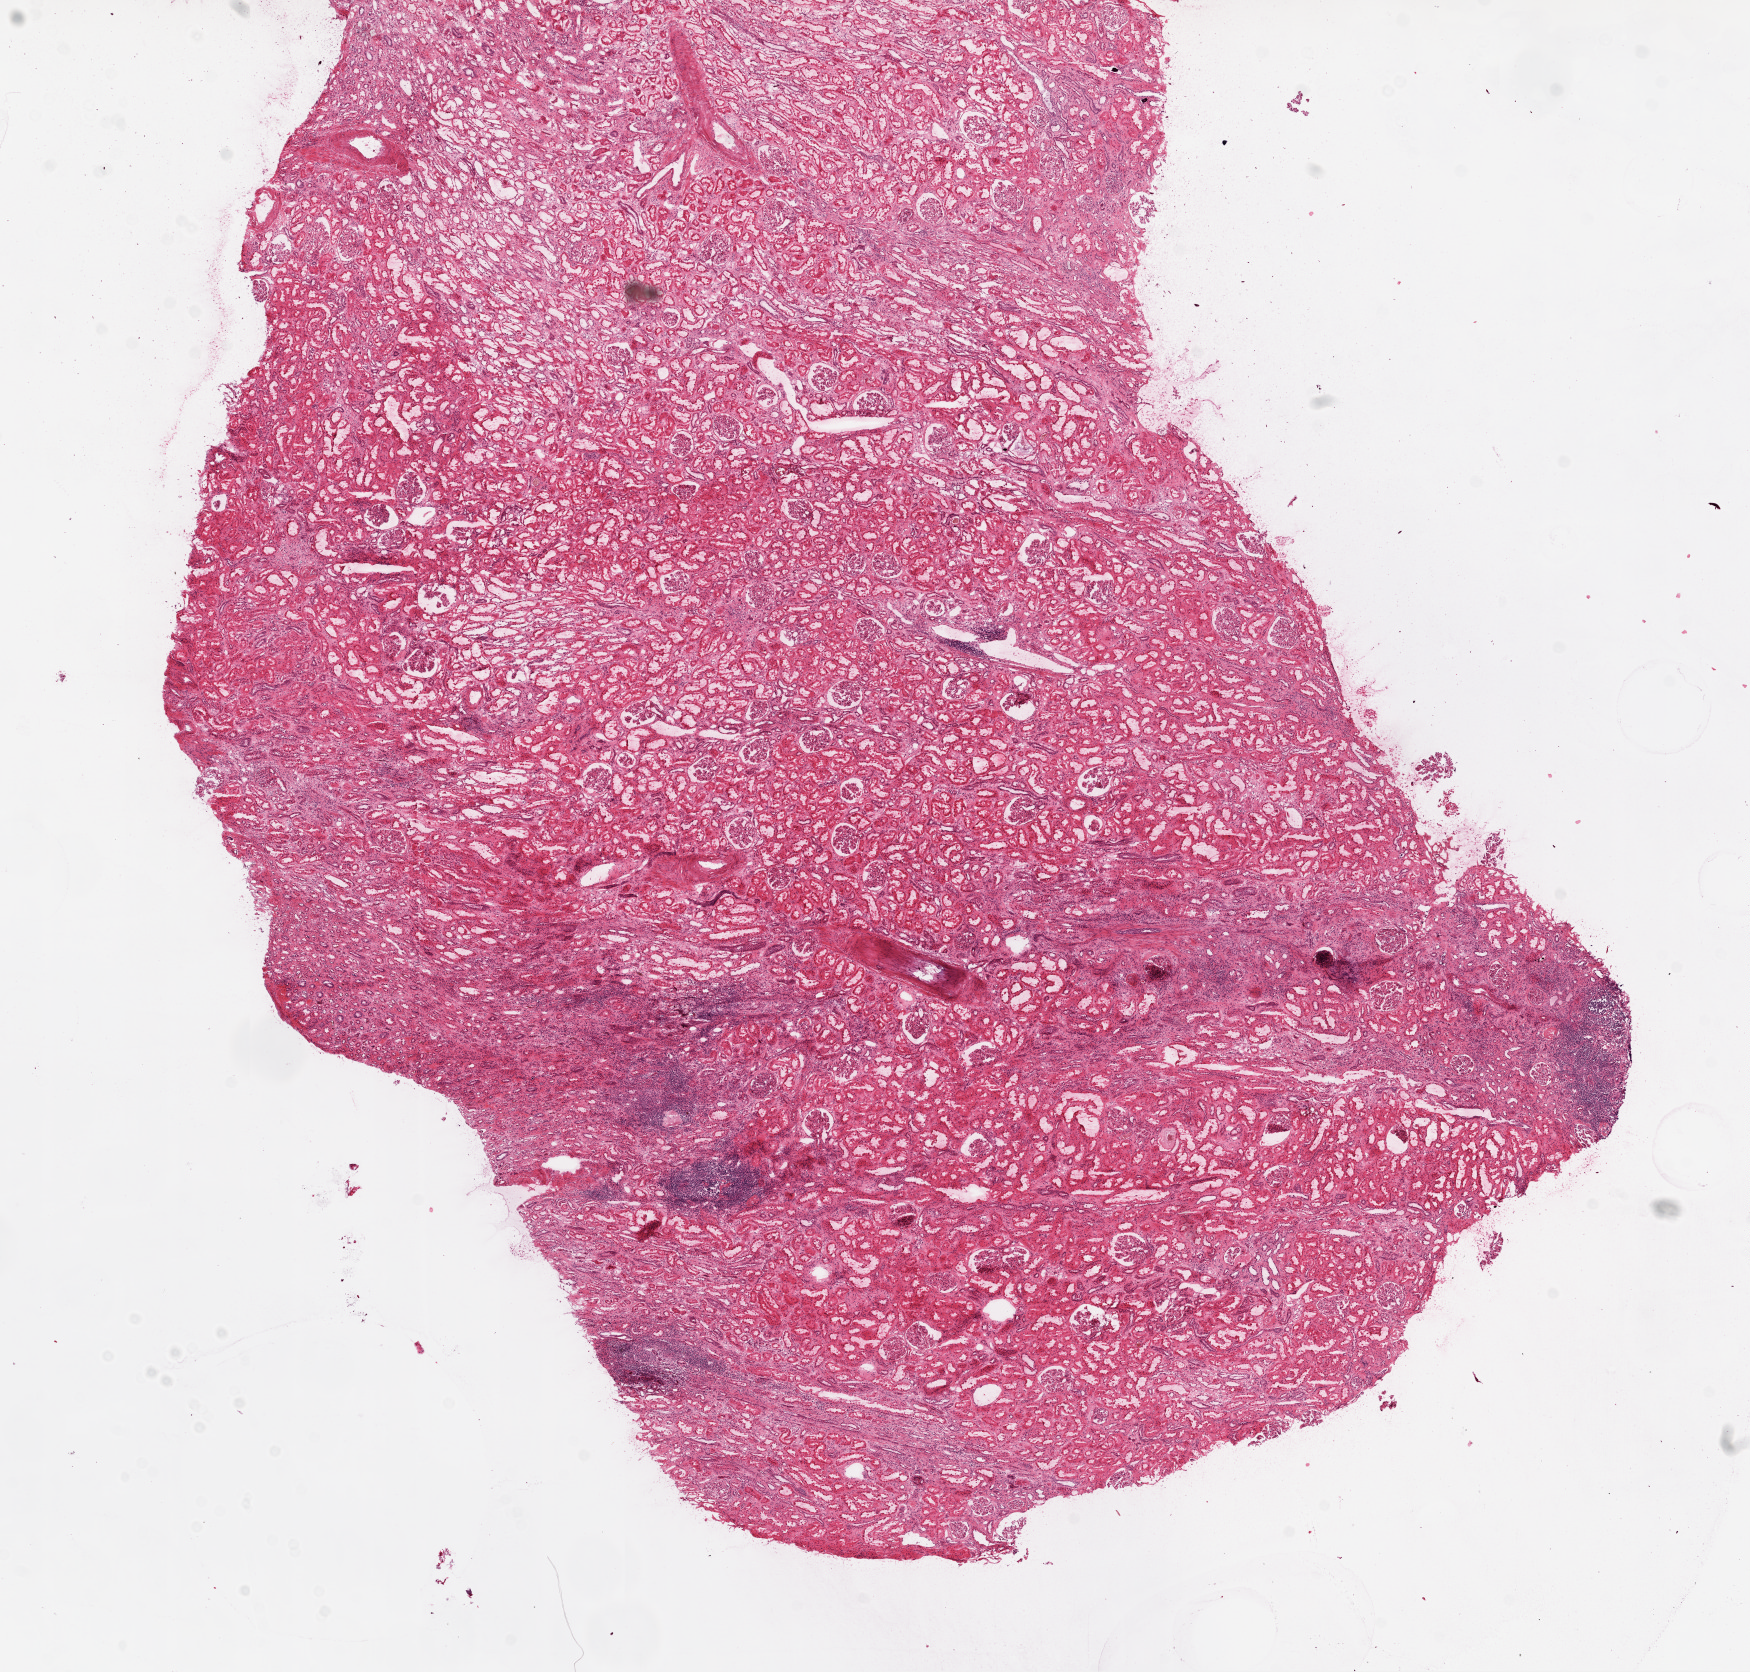
Hematoxylin and eosin (H&E) stained whole-slide image — shown as a low-resolution overview of the whole scanned area (about 14.0 x 13.4 mm); frozen section from the top of the tissue portion; solid tissue normal (non-tumour tissue) sample from the kidney. Patient: female, age at initial diagnosis 66 years.
• this section: solid tissue normal (non-tumour) sample from the same patient
• patient diagnosis: Clear cell adenocarcinoma, NOS